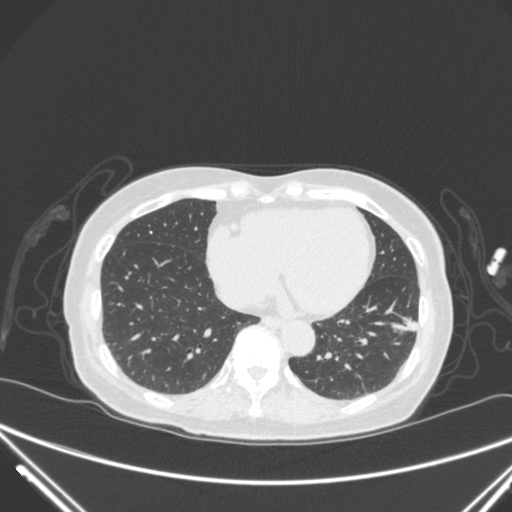
Chest CT, one axial slice. Slice 103 of 310 in the series (ordered by position). Lung window (W 1500 / L -600 HU). 512 × 512 image matrix, field of view 377 × 377 mm. Patient: female, 82 years. Case-level facts recorded for this patient, not image findings: clinical TNM (as recorded): T1c N0 M0; histopathological grade: G2.
Annotated regions visible in this slice (rectangle marked by the reading radiologist):
- lung tumour (recorded histology: adenocarcinoma): box from (x=385, y=307) to (x=428, y=349) px